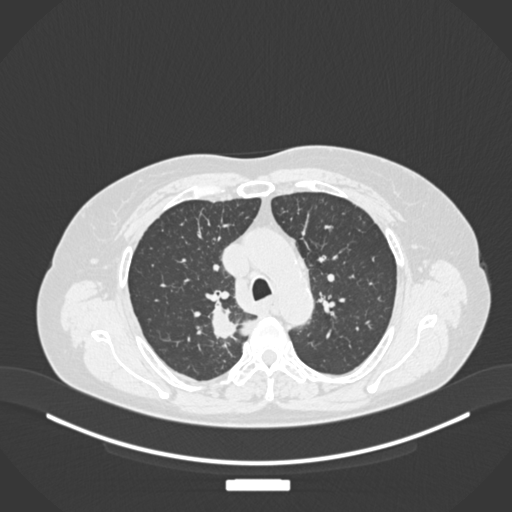
Chest CT, one axial slice; slice 183 of 237 in the series (ordered by position); reconstruction kernel B30f; lung window (W 1500 / L -600 HU); 512 × 512 image matrix, field of view 400 × 400 mm. Female patient, age 62 years. From the clinical record (not read from this slice): clinical TNM (as recorded): T1c N1 M0.
Structures marked on this image (bounding box drawn by a radiologist):
- lung tumour (recorded histology: squamous cell carcinoma): bounding box [x1, y1, x2, y2] px = [204, 298, 236, 343]